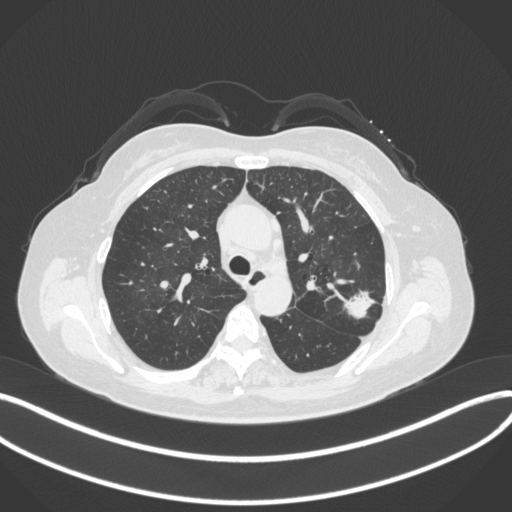
Chest CT, one axial slice. Position 236 of 330 along the scan axis. 120 kVp. Lung window (W 1500 / L -600 HU). 1 mm slice thickness. 512 × 512 image matrix. Patient: female, 60 years. Case-level facts recorded for this patient, not image findings: clinical TNM (as recorded): T1c N0 M0.
Structures marked on this image (rectangle marked by the reading radiologist):
- lung tumour (recorded histology: adenocarcinoma): bounding box <343,287,379,322> (left, top, right, bottom; pixels)